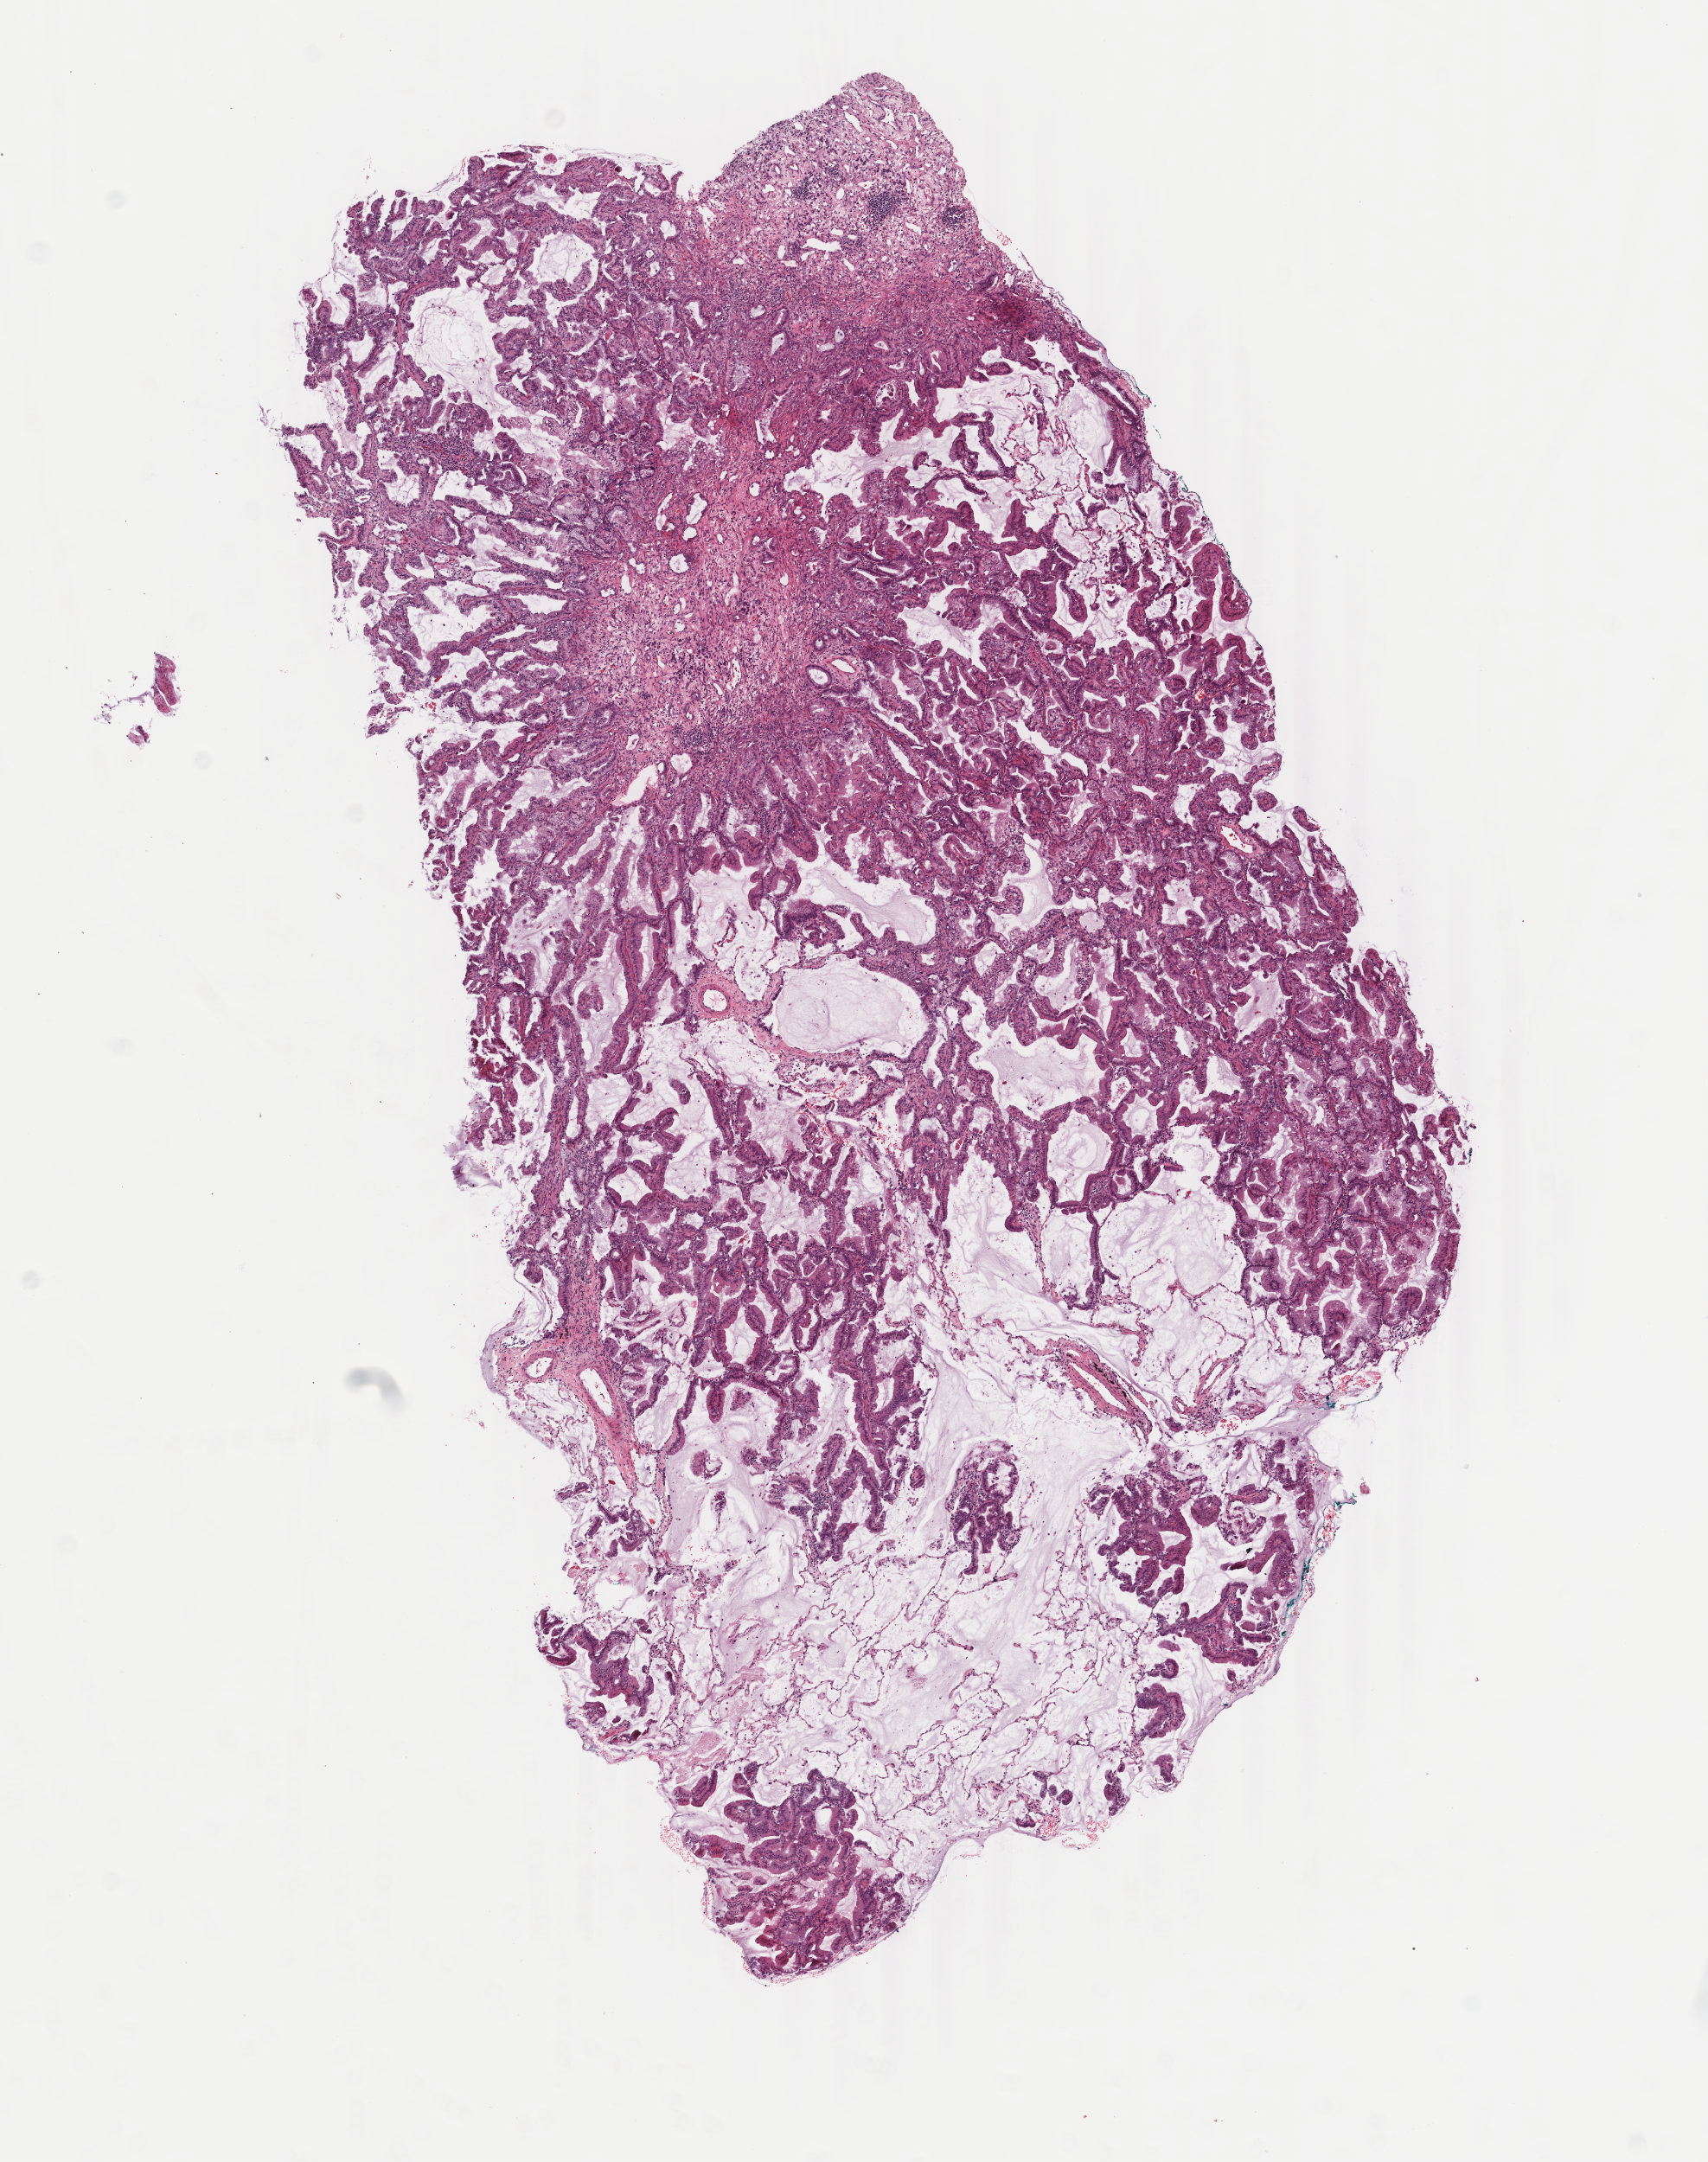
H&E-stained whole-slide image — low-resolution overview of the scanned area, about 7.9 x 9.9 mm (from a 40x scan), frozen section from the bottom of the tissue portion, primary tumour sample from the lung. Male, age 64 years at initial diagnosis. Slide review estimates, as recorded: tumour cells 80%, tumour nuclei 80%, normal cells 0%, stromal cells 20%, necrosis 0%. Infiltration values recorded for this section: lymphocyte infiltration 12%, monocyte infiltration 3%, neutrophil infiltration 1%.
- histologic diagnosis: Mucinous adenocarcinoma (lower lobe, lung)
- TNM: T3 N0 M0
- AJCC pathologic stage: IIB (7th edition)